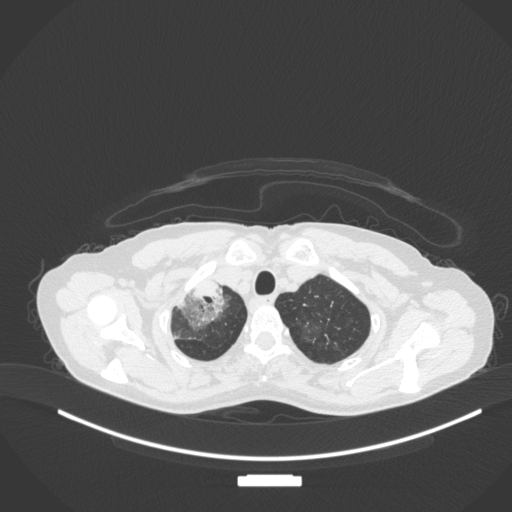
Chest CT, one axial slice; position 287 of 311 along the scan axis; reconstruction kernel B31f; lung window (W 1500 / L -600 HU); 512 × 512 image matrix. Female patient, age 59 years. From the clinical record (not read from this slice): clinical TNM (as recorded): T3 N0 M0; histopathological grade: G1.
Structures marked on this image (rectangle marked by the reading radiologist):
- lung tumour (recorded histology: adenocarcinoma): bounding box [x1, y1, x2, y2] px = [175, 273, 226, 330]